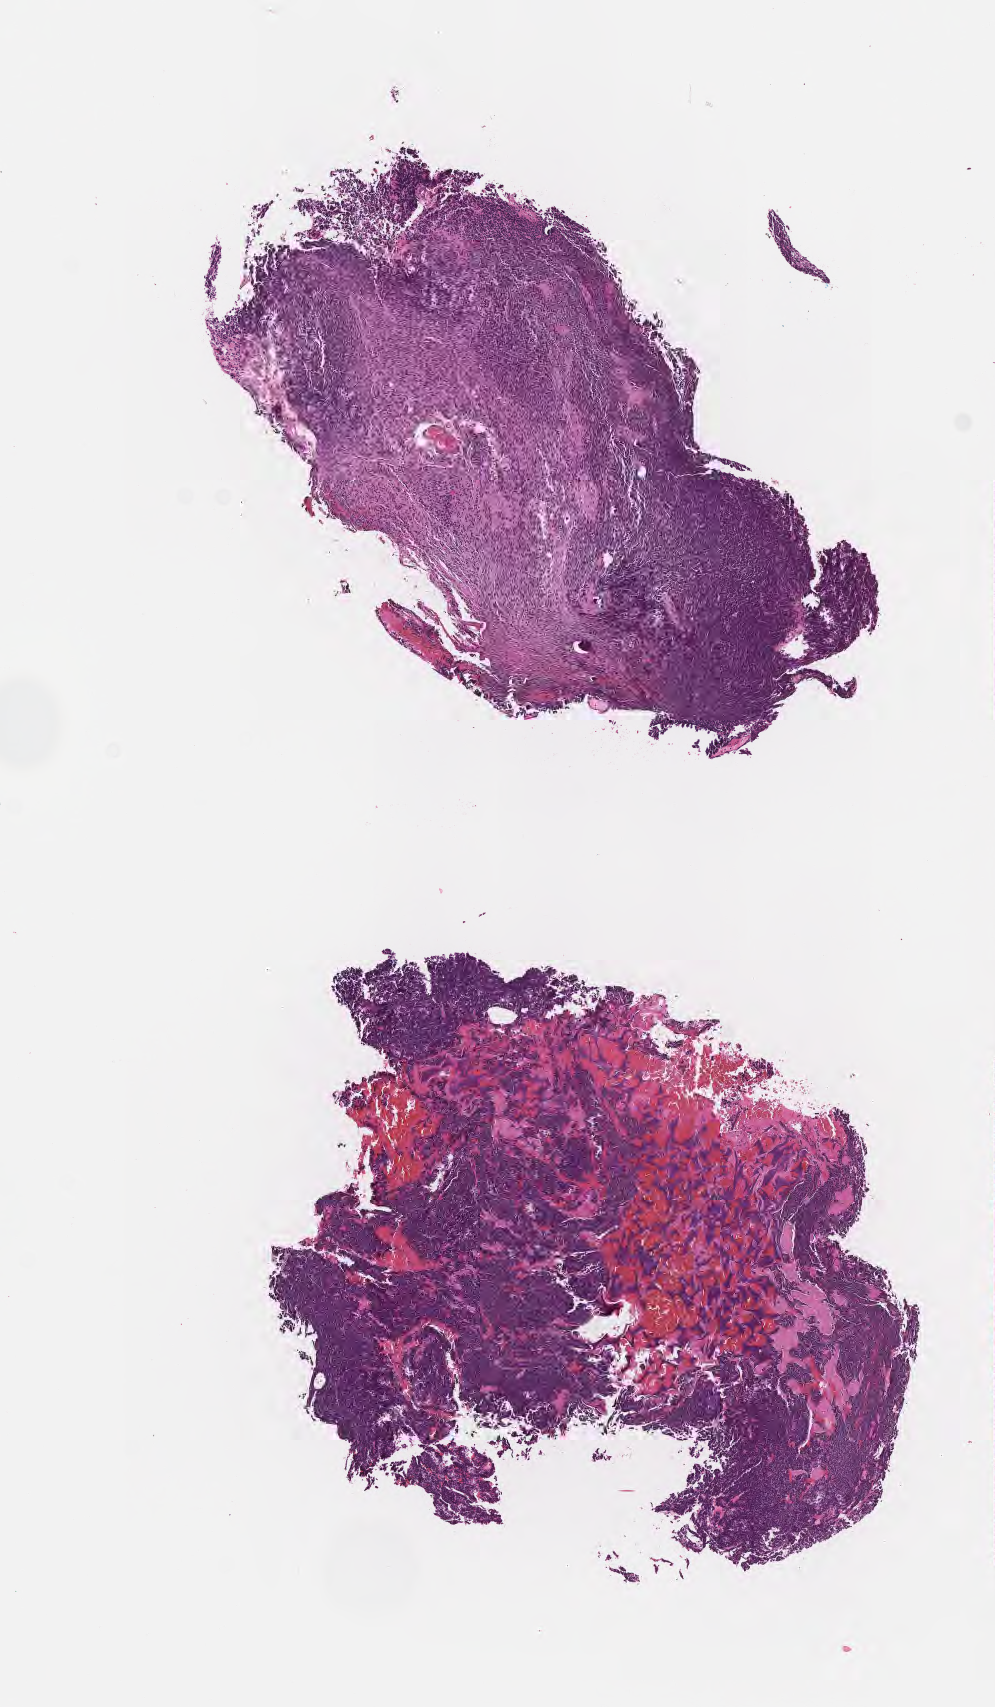
Hematoxylin and eosin (H&E) whole-slide image of tumor tissue from the brain, whole scanned area (about 4.0 x 6.9 mm) shown as a low-resolution overview; formalin-fixed, paraffin-embedded (FFPE) tissue. Patient: male, age 129 months (10 years 9 months).
Diagnosis: Pinealoma.